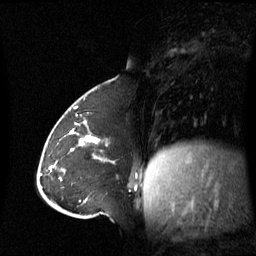
Breast MRI (dynamic contrast-enhanced), one sagittal slice; position 23 of 60 along the scan axis; dynamic contrast-enhanced series, image 2 of 3 at this slice position (ordered by acquisition); 1.5 T; TE 4.2 ms, TR 8.4 ms; 2.8 mm slice thickness; 256 × 256 image matrix, field of view 270 × 270 mm. Female patient, age 43 years. From the clinical record (not read from this slice): setting: breast cancer imaged before/during neoadjuvant chemotherapy; receptor status: triple-negative.
Annotated regions visible in this slice (semi-automatically segmented with operator editing):
- analysis volume of interest (the breast-tissue region the enhancement analysis was run in; not a lesion): bounding box <62,124,137,180> (left, top, right, bottom; pixels)
- tumour enhancement mask (voxels above the 70 % enhancement threshold inside the analysis volume of interest): <69,129,137,176>